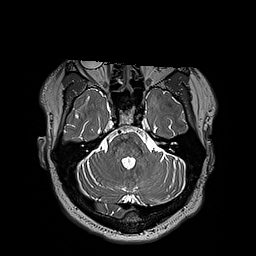
Brain MRI from a brain-tumour surgery series, one axial slice; position 135 of 192 along the scan axis; 1 mm slice thickness; 256 × 256 image matrix, field of view 250 × 250 mm. Case-level facts recorded for this patient, not image findings: histopathology: Astrocytoma; WHO grade: 3; IDH mutation: yes; tumour location: Left Insular.
Structures marked on this image (manually delineated by an expert):
- tumour: box from (x=151, y=98) to (x=155, y=101) px